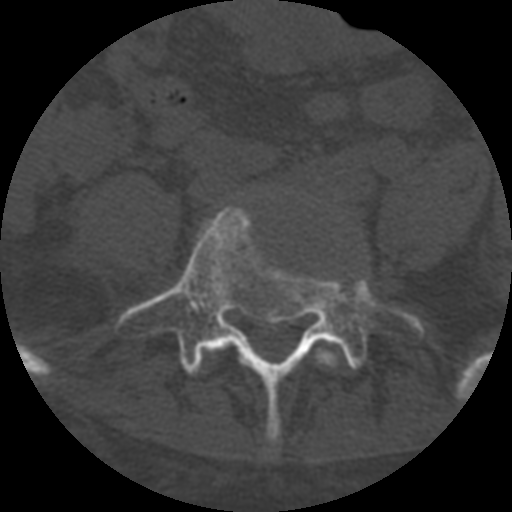
CT including the spine, one axial slice. Position 190 of 708 along the scan axis. Reconstruction kernel STANDARD. 120 kVp. One of 3 acquisitions stored at this slice position. Bone window (W 1800 / L 400 HU). 1.25 mm slice thickness. 512 × 512 image matrix. Patient age 55 years. From the clinical record (not read from this slice): primary cancer: colon; vertebrae with lytic lesions (as recorded): T12, L1, L5.
Structures marked on this image (semi-automatic segmentation, software-assisted and operator-edited):
- L4 vertebra: bounding box <221,341,341,367> (left, top, right, bottom; pixels)
- L5 vertebra: <116,206,424,439>